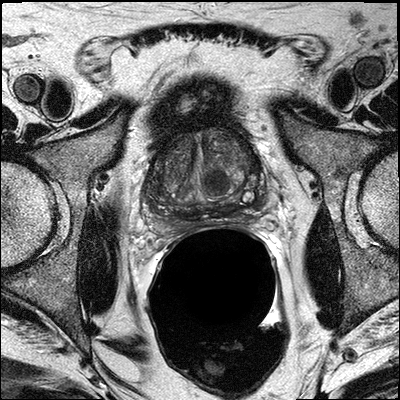
MRI of the prostate; 3 images, each a single mid-volume slice chosen by position (not for content).
Image 1: axial T2-weighted image, slice 17 of 32, 3 mm slice thickness.
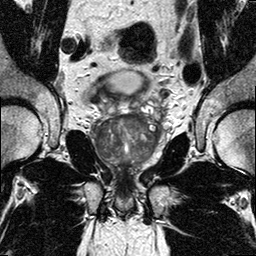
Image 2: coronal T2-weighted image, series "T2W_TSE_COR", slice 13 of 24, 3 mm slice thickness.
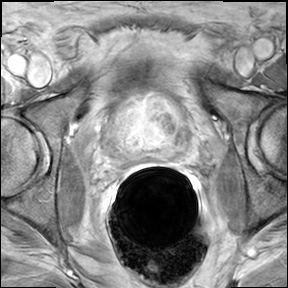
Image 3: DCE (dynamic gadolinium-enhanced) axial slice, slice 17 of 32, dynamic phase 5 of 8.
Radiologist's MRI report for this examination:
FINDINGS: The prostate has a maximal lateral diameter of 5.6cm, a maximal cranio-caudal diameter of 4.2cm and a maximal AP diameter of 4.5 cm resulting in an estimated gland volume of 55 cc. The zonal anatomy is preserved. The central gland shows moderate BPH. In the right peripheral zone, posterior lateral, from 7-9 o'clock, in the mid third of the prostate with extension into the base there is a 2.4 x 0.9 cm tumor seen. The pseudocapsule at the right neurovascular bundle cannot be delineated continuously and appears irregular; Within the neurovascular bundle itself no manifest tumor mass seen. In the left peripheral zone ,within the apical third, (with extension to the midthird) and in predominantly in the left apex, there is a second mass seen between 3-6 o'clock, measuring 1.9 x 1.6 cm. At 9:00 at the apex this tumor mass cannot be delineated from the pubo-rectal sling/superior edge of the internal sphincter and abuts the urethra. At this point no extraprostatic disease visualized. However, tumor extents to apical margin and lateral margin of the gland. Extraprostatic extension is to be expected soon. No evidence for involvement of the neurovascular bundle on the left side. No evidence for seminal vesicles infiltration. No evidence of involvement of bladder neck and rectal wall. No suspiciously enlarged obturator and iliac lymph nodes. There is a 4 x 7 mm perirectal lymph node seen at 10 o'clock, one centimeter posterior to the right seminal vesicles. IMPRESSION: 1) Bilateral Prostate Cancer with a dominant mass in the right posterior lateral mid-third of the prostate, and a second dominant mass in the left apex. 2) Beginning capsular infiltration at the right neurovascular bundle likely, without manifest extracapsular disease. If nerve sparing is performed, right side should be excluded, left sided nerve sparing is possible. 3) No definite extraprostatic extension at the left apex, however, tumor mass reaches the margins of the gland apical and lateral. 4) Oval 4 x 7 mm right perirectal lymph node at 10 o'clock; just one cm posterior to the right seminal vesicles. This is an unspecific finding. Otherwise, no enlarged or suspicious obturator or iliac lymph nodes on either side. 5) No Seminal vesicles infiltration, no involvement of Urinary bladder or rectum.

Biopsy pathology report for this patient (as recorded):
1-RIGHT PZ: PROSTATIC ADENOCARCINOMA, GLEASON SCORE 3+3=6/10 INVOLVING 40% OF THE TISSUE REPRESENTED. 2-RIGHT PZ/TZ: PROSTATIC ADENOCARCINOMA, GLEASON SCORE 3+3=6/10 INVOLVING 50% OF THE TISSUE REPRESENTED. 3-RIGHT APEX: PROSTATIC TISSUE, NO TUMOR IDENTIFIED. 4-LEFT PZ: PROSTATIC ADENOCARCINOMA, GLEASON SCORE 3+4=7/10 INVOLVING 60% OF THE TISSUE REPRESENTED. 5-LEFT PZ/TZ: PROSTATIC ADENOCARCINOMA, GLEASON SCORE 3+3=6/10 INVOLVING 30% OF THE TISSUE REPRESENTED. 6-LEFT APEX: PROSTATIC ADENOCARCINOMA, GLEASON SCORE 3+3=6/10 INVOLVING 15% OF THE TISSUE REPRESENTED.